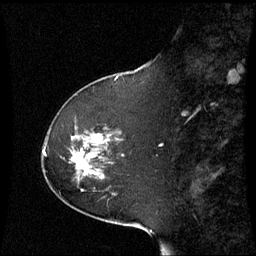
Breast MRI (dynamic contrast-enhanced), one sagittal slice. Position 21 of 60 along the scan axis. Dynamic contrast-enhanced series, image 2 of 3 at this slice position (ordered by acquisition). 1.5 T. TE 4.2 ms, TR 8.9 ms. 2.4 mm slice thickness. 256 × 256 image matrix, field of view 230 × 230 mm. Female patient, age 51 years. From the clinical record (not read from this slice): setting: breast cancer imaged before/during neoadjuvant chemotherapy; receptor status: HR-positive, HER2-negative.
Annotated regions visible in this slice (semi-automatic segmentation, software-assisted and operator-edited):
- analysis volume of interest (the breast-tissue region the enhancement analysis was run in; not a lesion): bounding box (x1, y1, x2, y2) in pixels: (43, 127, 113, 191)
- tumour enhancement mask (voxels above the 70 % enhancement threshold inside the analysis volume of interest): (71, 136, 102, 172)